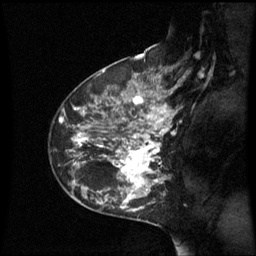
Breast MRI (dynamic contrast-enhanced), one sagittal slice; position 39 of 60 along the scan axis; dynamic contrast-enhanced series, image 2 of 3 at this slice position (ordered by acquisition); 1.5 T; TE 4.2 ms, TR 8.9 ms; 2.4 mm slice thickness; 256 × 256 image matrix, field of view 210 × 210 mm. Patient: female, 42 years. Case-level facts recorded for this patient, not image findings: setting: breast cancer imaged before/during neoadjuvant chemotherapy; receptor status: HER2-positive.
Annotated regions visible in this slice (semi-automatically segmented with operator editing):
- analysis volume of interest (the breast-tissue region the enhancement analysis was run in; not a lesion): bounding box <62,93,171,210> (left, top, right, bottom; pixels)
- tumour enhancement mask (voxels above the 70 % enhancement threshold inside the analysis volume of interest): <75,95,171,209>